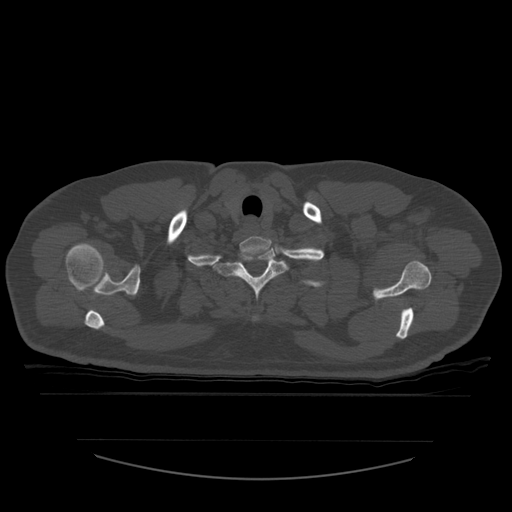
CT including the spine, one axial slice. Position 470 of 532 along the scan axis. 120 kVp. Bone window (W 1800 / L 400 HU). 1.25 mm slice thickness. 512 × 512 image matrix, field of view 441 × 441 mm. Patient age 44 years. From the clinical record (not read from this slice): primary cancer: soft tissue sarcoma.
Outlined on this slice (semi-automatically segmented with operator editing):
- T1 vertebra: box from (x=214, y=247) to (x=288, y=321) px
- T2 vertebra: (x=305, y=283)–(x=312, y=286)